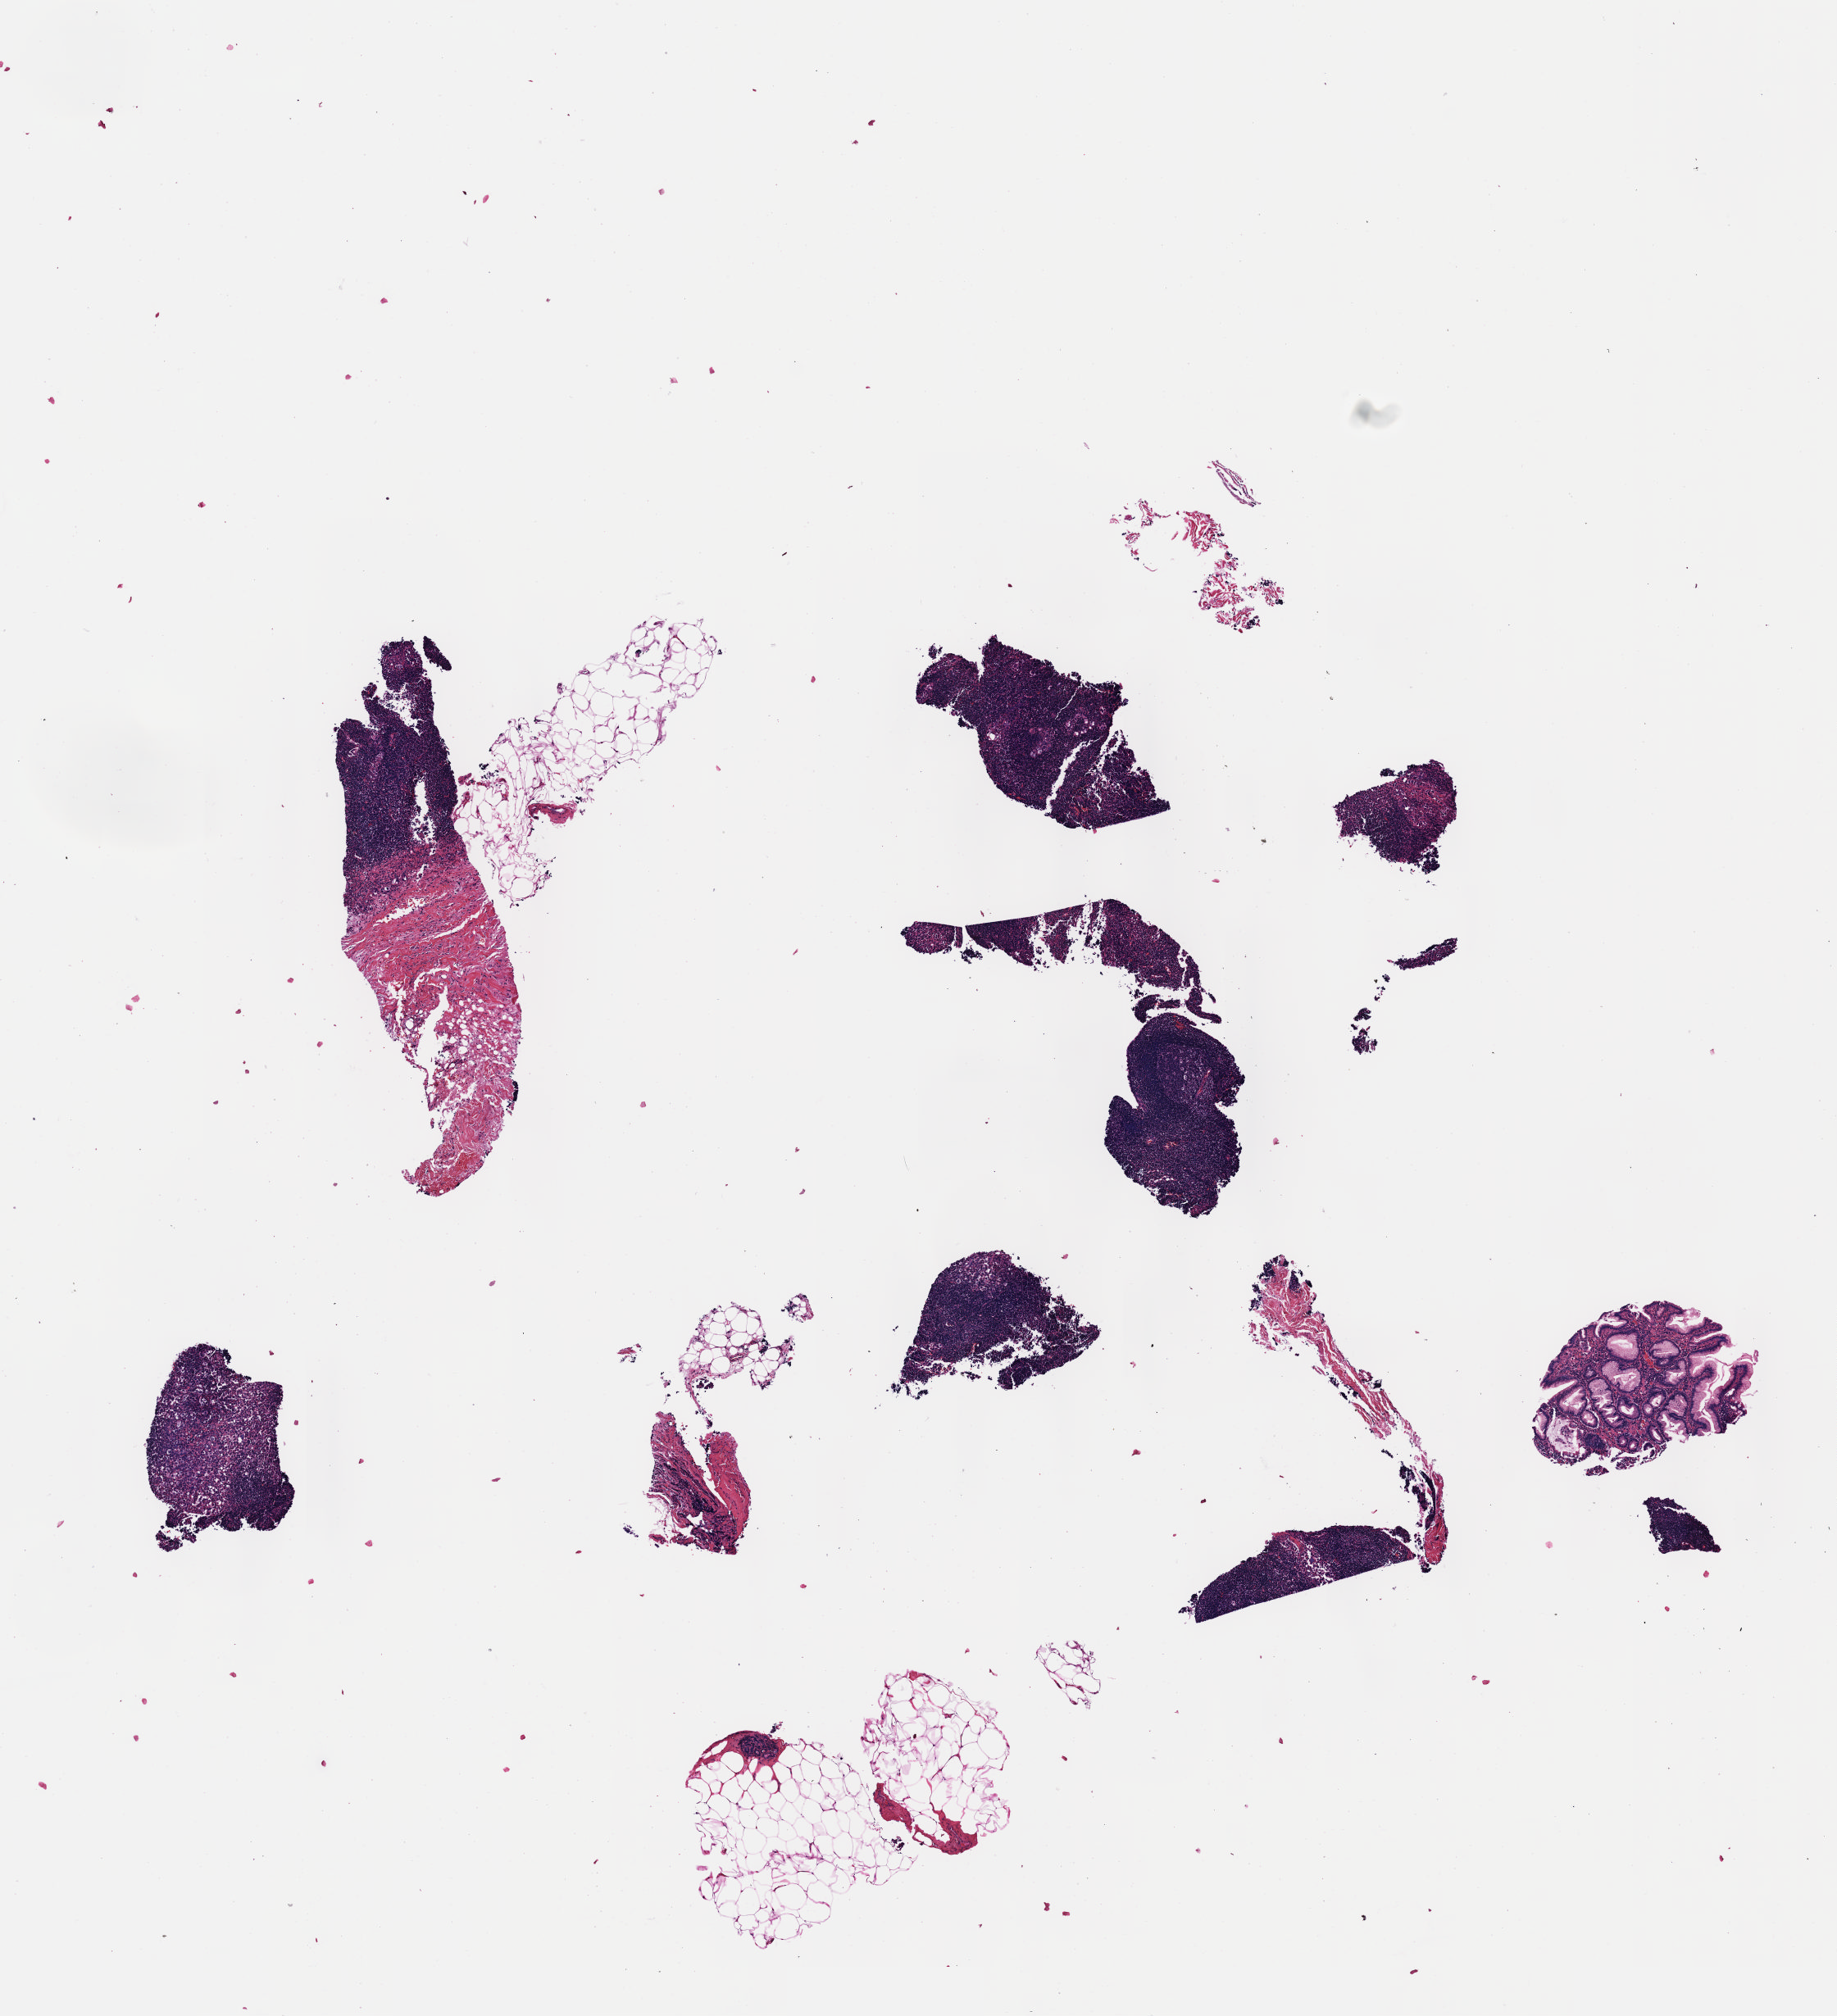
Whole-slide histology image, H&E-stained — whole scanned area (about 9.1 x 9.9 mm) shown as a low-resolution overview; formalin-fixed paraffin-embedded (FFPE) diagnostic section; sample: primary tumour, breast. Female, age 36 years at initial diagnosis.
- AJCC pathologic stage: IIIA
- TNM: T2 N2 M0
- histologic diagnosis: Infiltrating duct carcinoma, NOS
- lymph nodes positive (case pathology): 1 of 14 examined